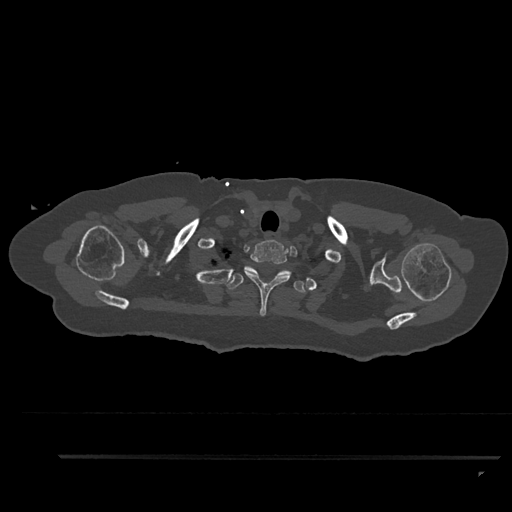
CT including the spine, one axial slice. Slice 748 of 797 in the series (ordered by position). 120 kVp. Bone window (W 1800 / L 400 HU). 0.5 mm slice thickness. 512 × 512 image matrix, field of view 408 × 408 mm. Patient: female, 44 years. From the clinical record (not read from this slice): primary cancer: renal; vertebrae with lytic lesions (as recorded): L1.
Annotated regions visible in this slice (semi-automatically segmented with operator editing):
- T1 vertebra: bounding box <242,240,291,316> (left, top, right, bottom; pixels)
- T2 vertebra: <227,267,306,293>